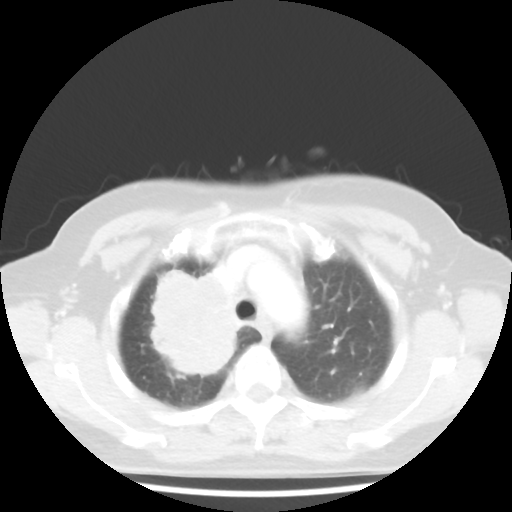
Chest CT, one axial slice; position 35 of 44 along the scan axis; 100 kVp; lung window (W 1500 / L -600 HU); 5 mm slice thickness; 512 × 512 image matrix, field of view 316 × 316 mm. Female patient, age 62 years. From the clinical record (not read from this slice): clinical TNM (as recorded): T3 N0 M0; histopathological grade: G3.
Outlined on this slice (rectangle marked by the reading radiologist):
- lung tumour (recorded histology: small cell carcinoma): bounding box [x1, y1, x2, y2] px = [139, 256, 250, 385]